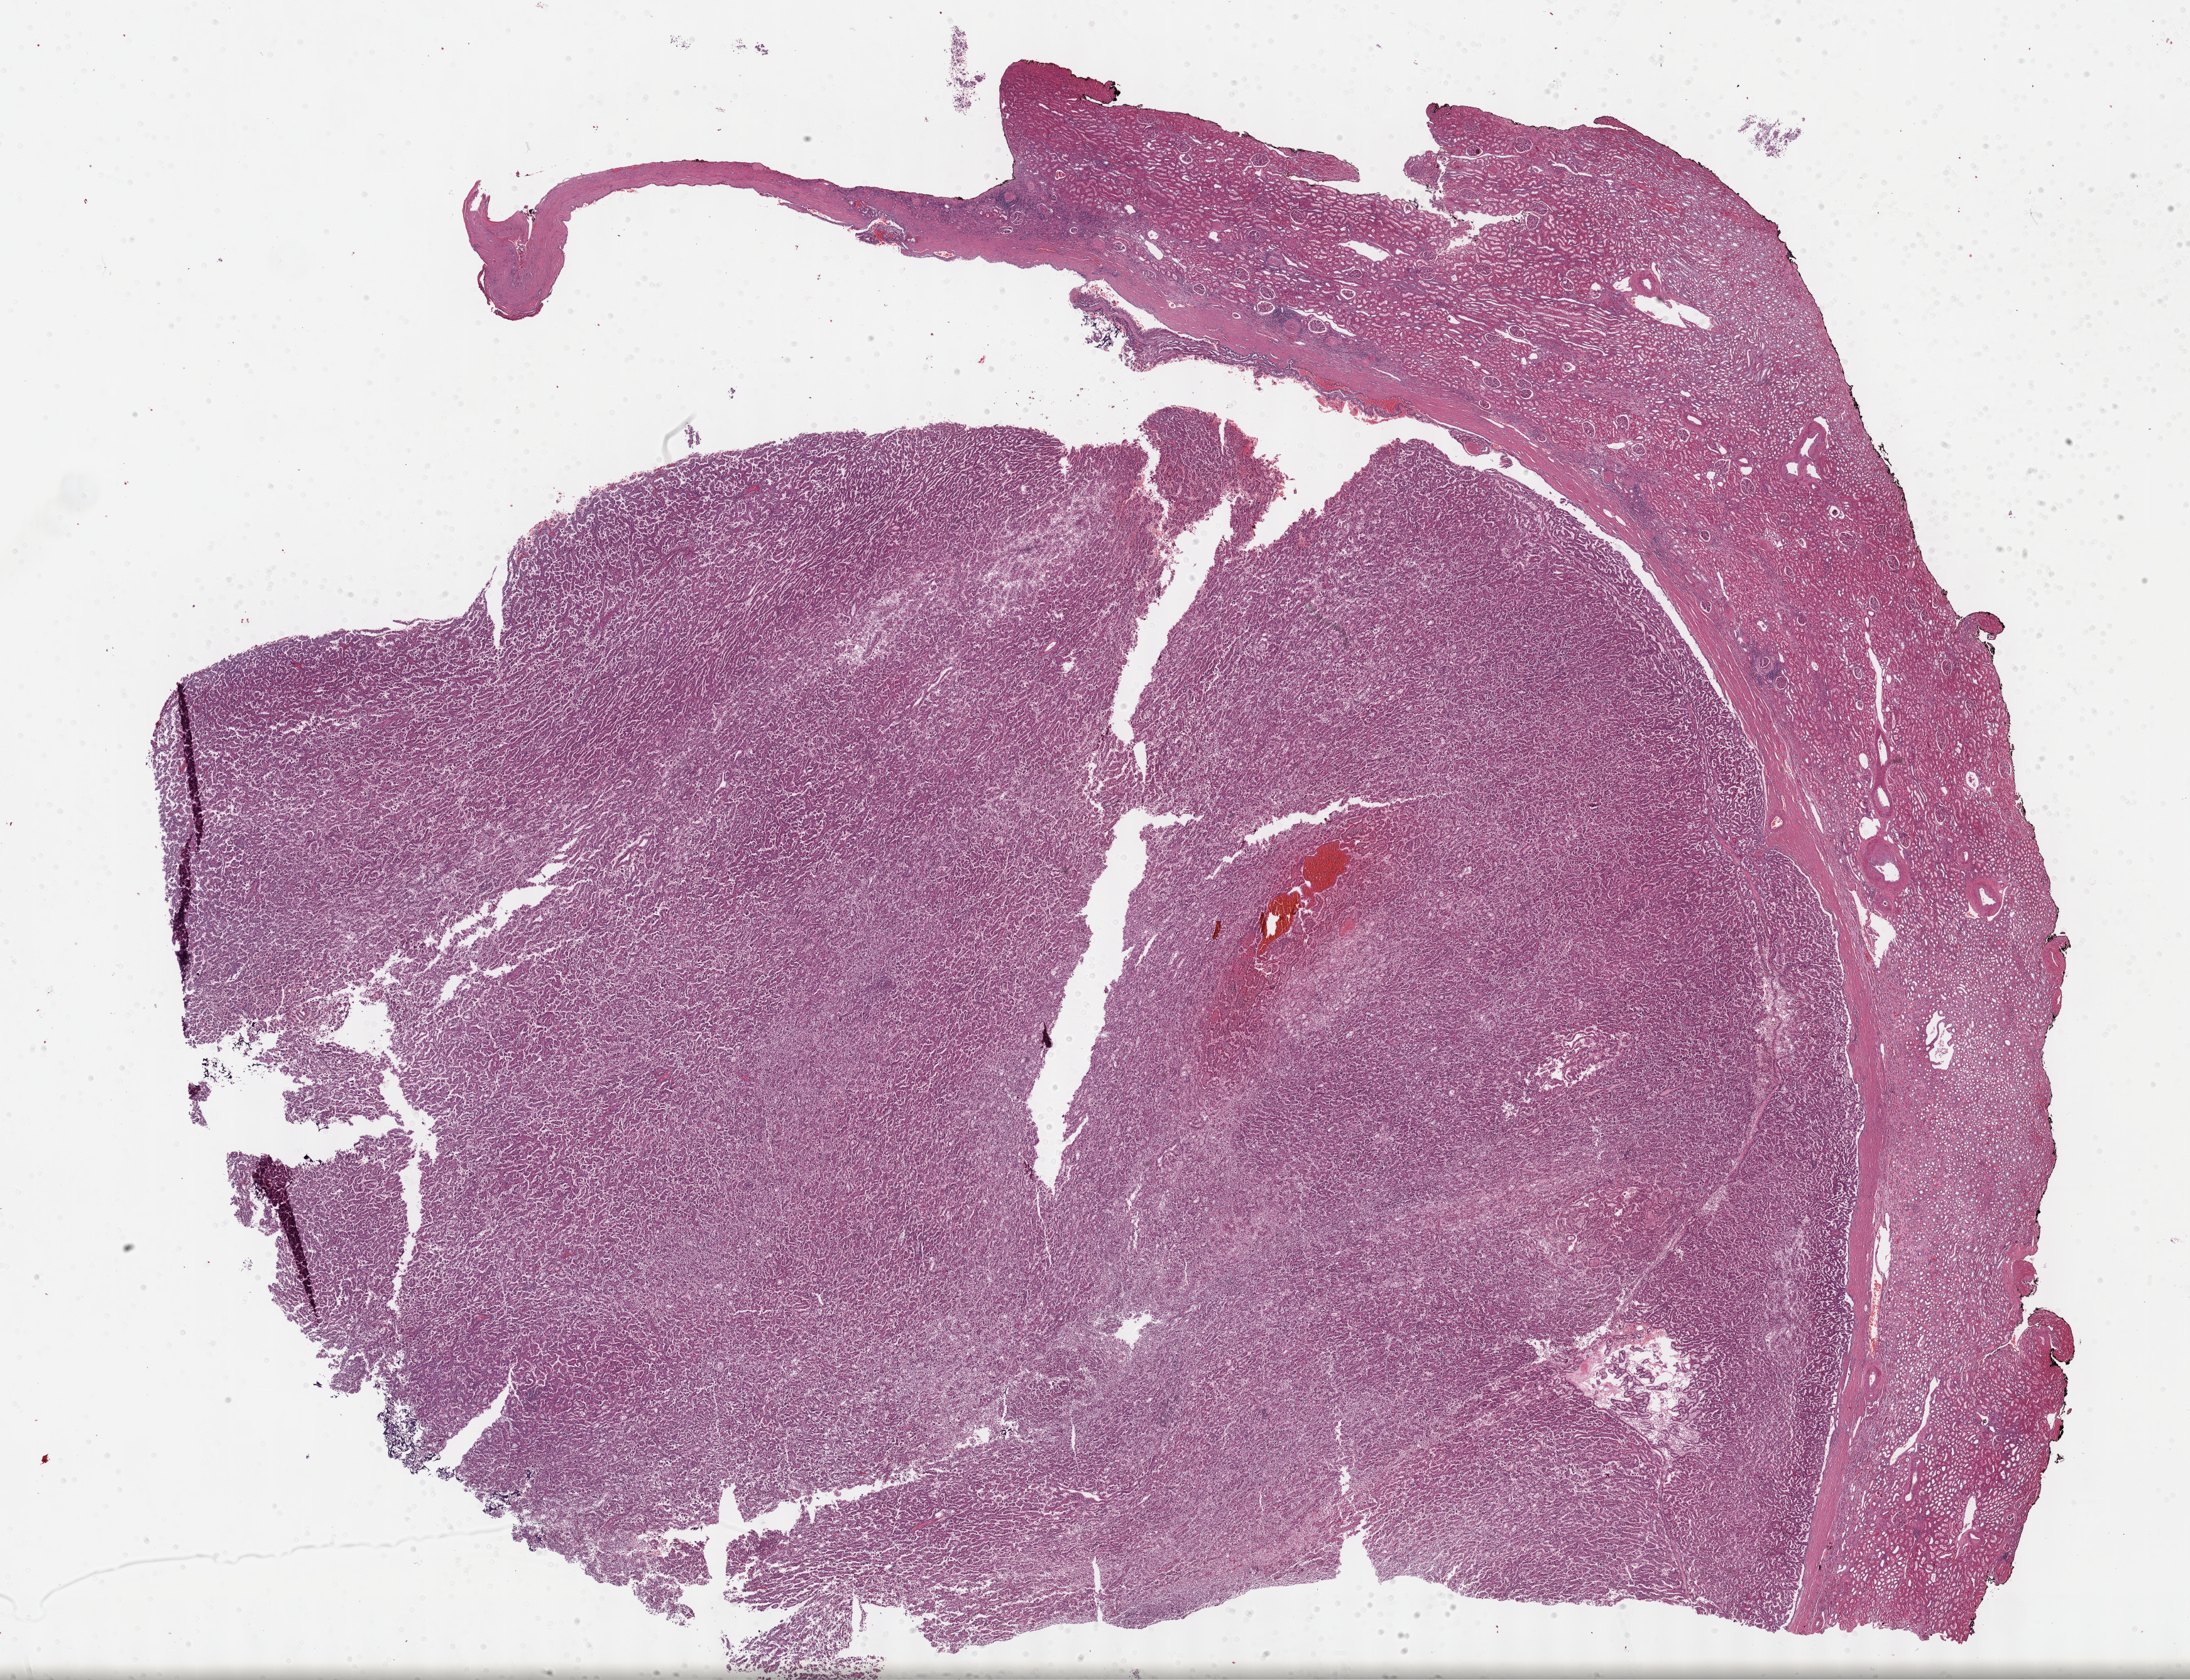
H&E whole-slide image — low-resolution overview of the scanned area, about 28.2 x 21.6 mm (slide scanned at 40x), FFPE section, sample: primary tumour, kidney. Patient: male, age at initial diagnosis 50 years.
Pathologic diagnosis: Papillary adenocarcinoma, NOS. AJCC pathologic stage: I (7th edition).